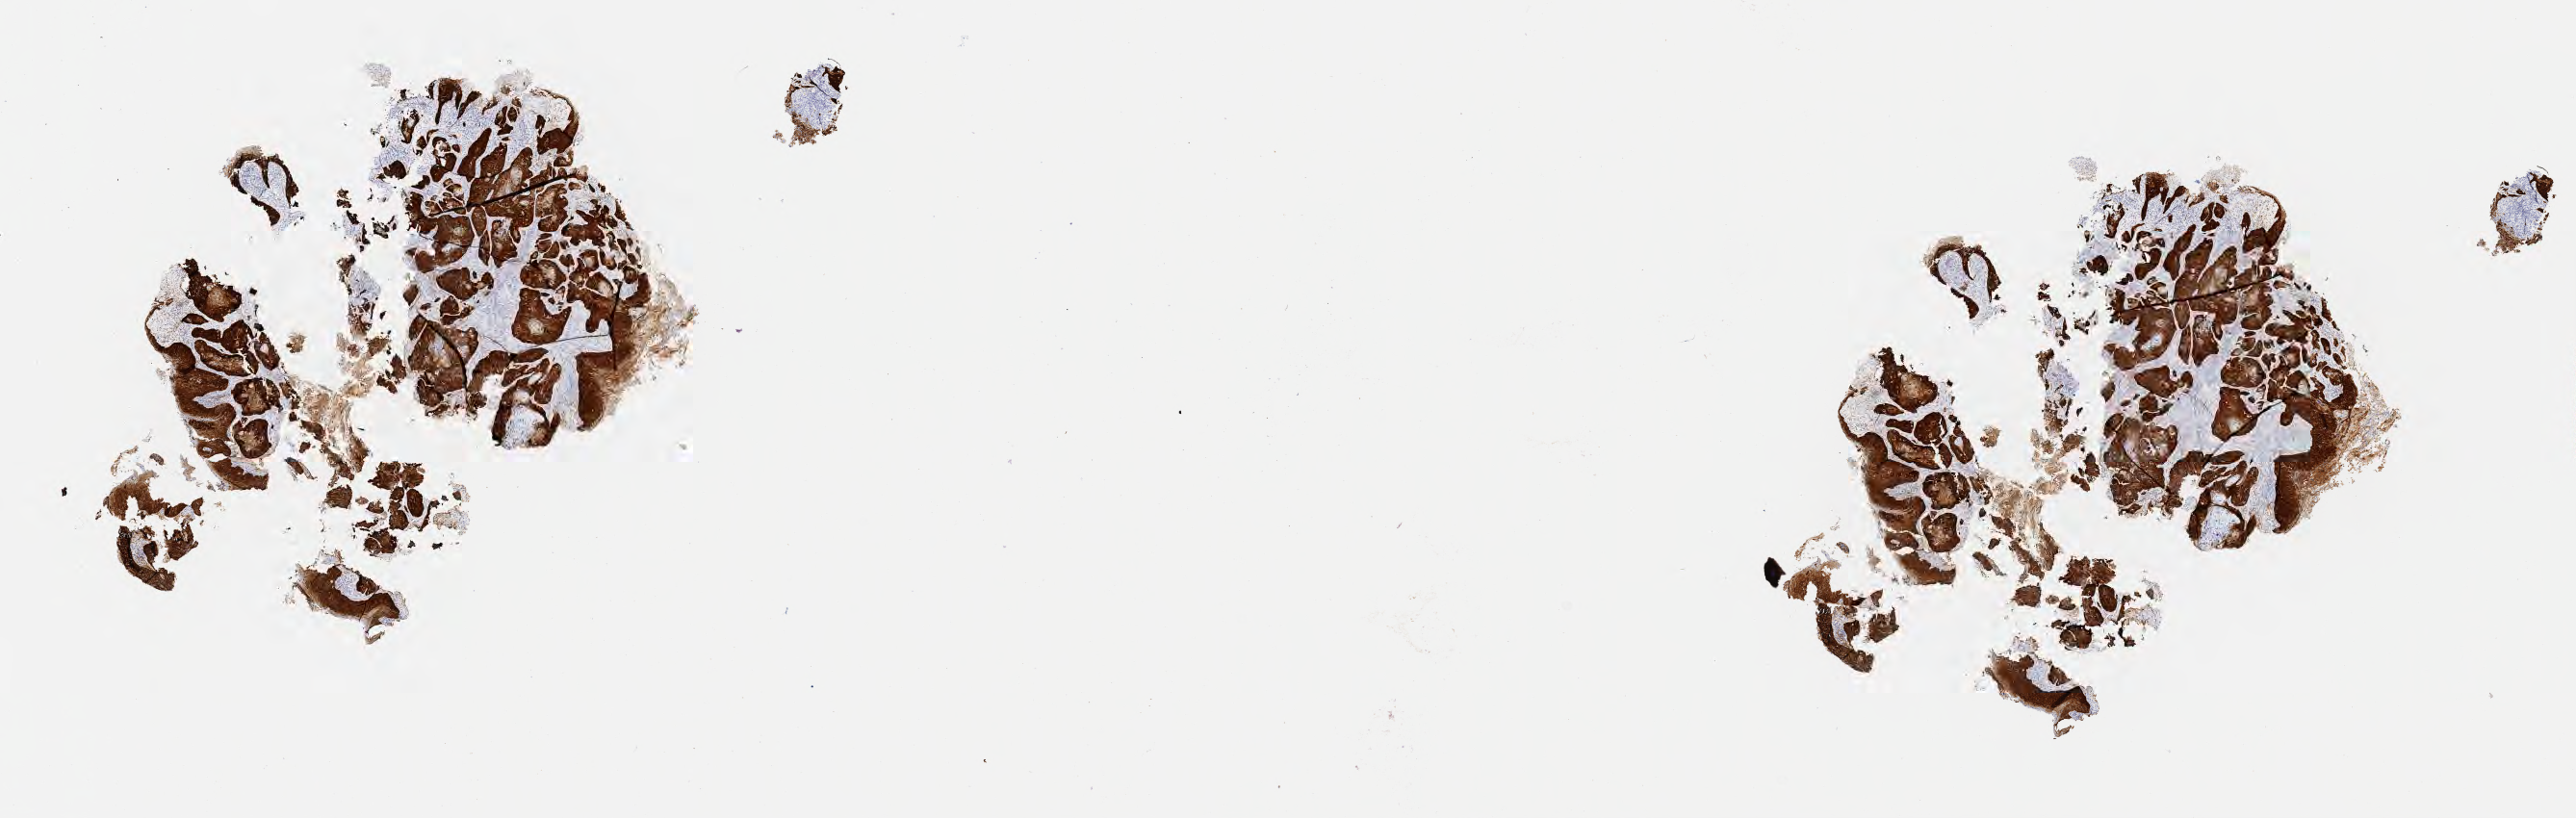
Whole-slide image, immunohistochemical stain for p16 (p16INK4a) — a low-resolution overview of the entire scanned area, about 21.6 x 6.9 mm. Specimen: tumor tissue. Site: cervix. Patient: female, age 59 years.
Diagnosis: Squamous cell carcinoma, keratinizing, NOS.